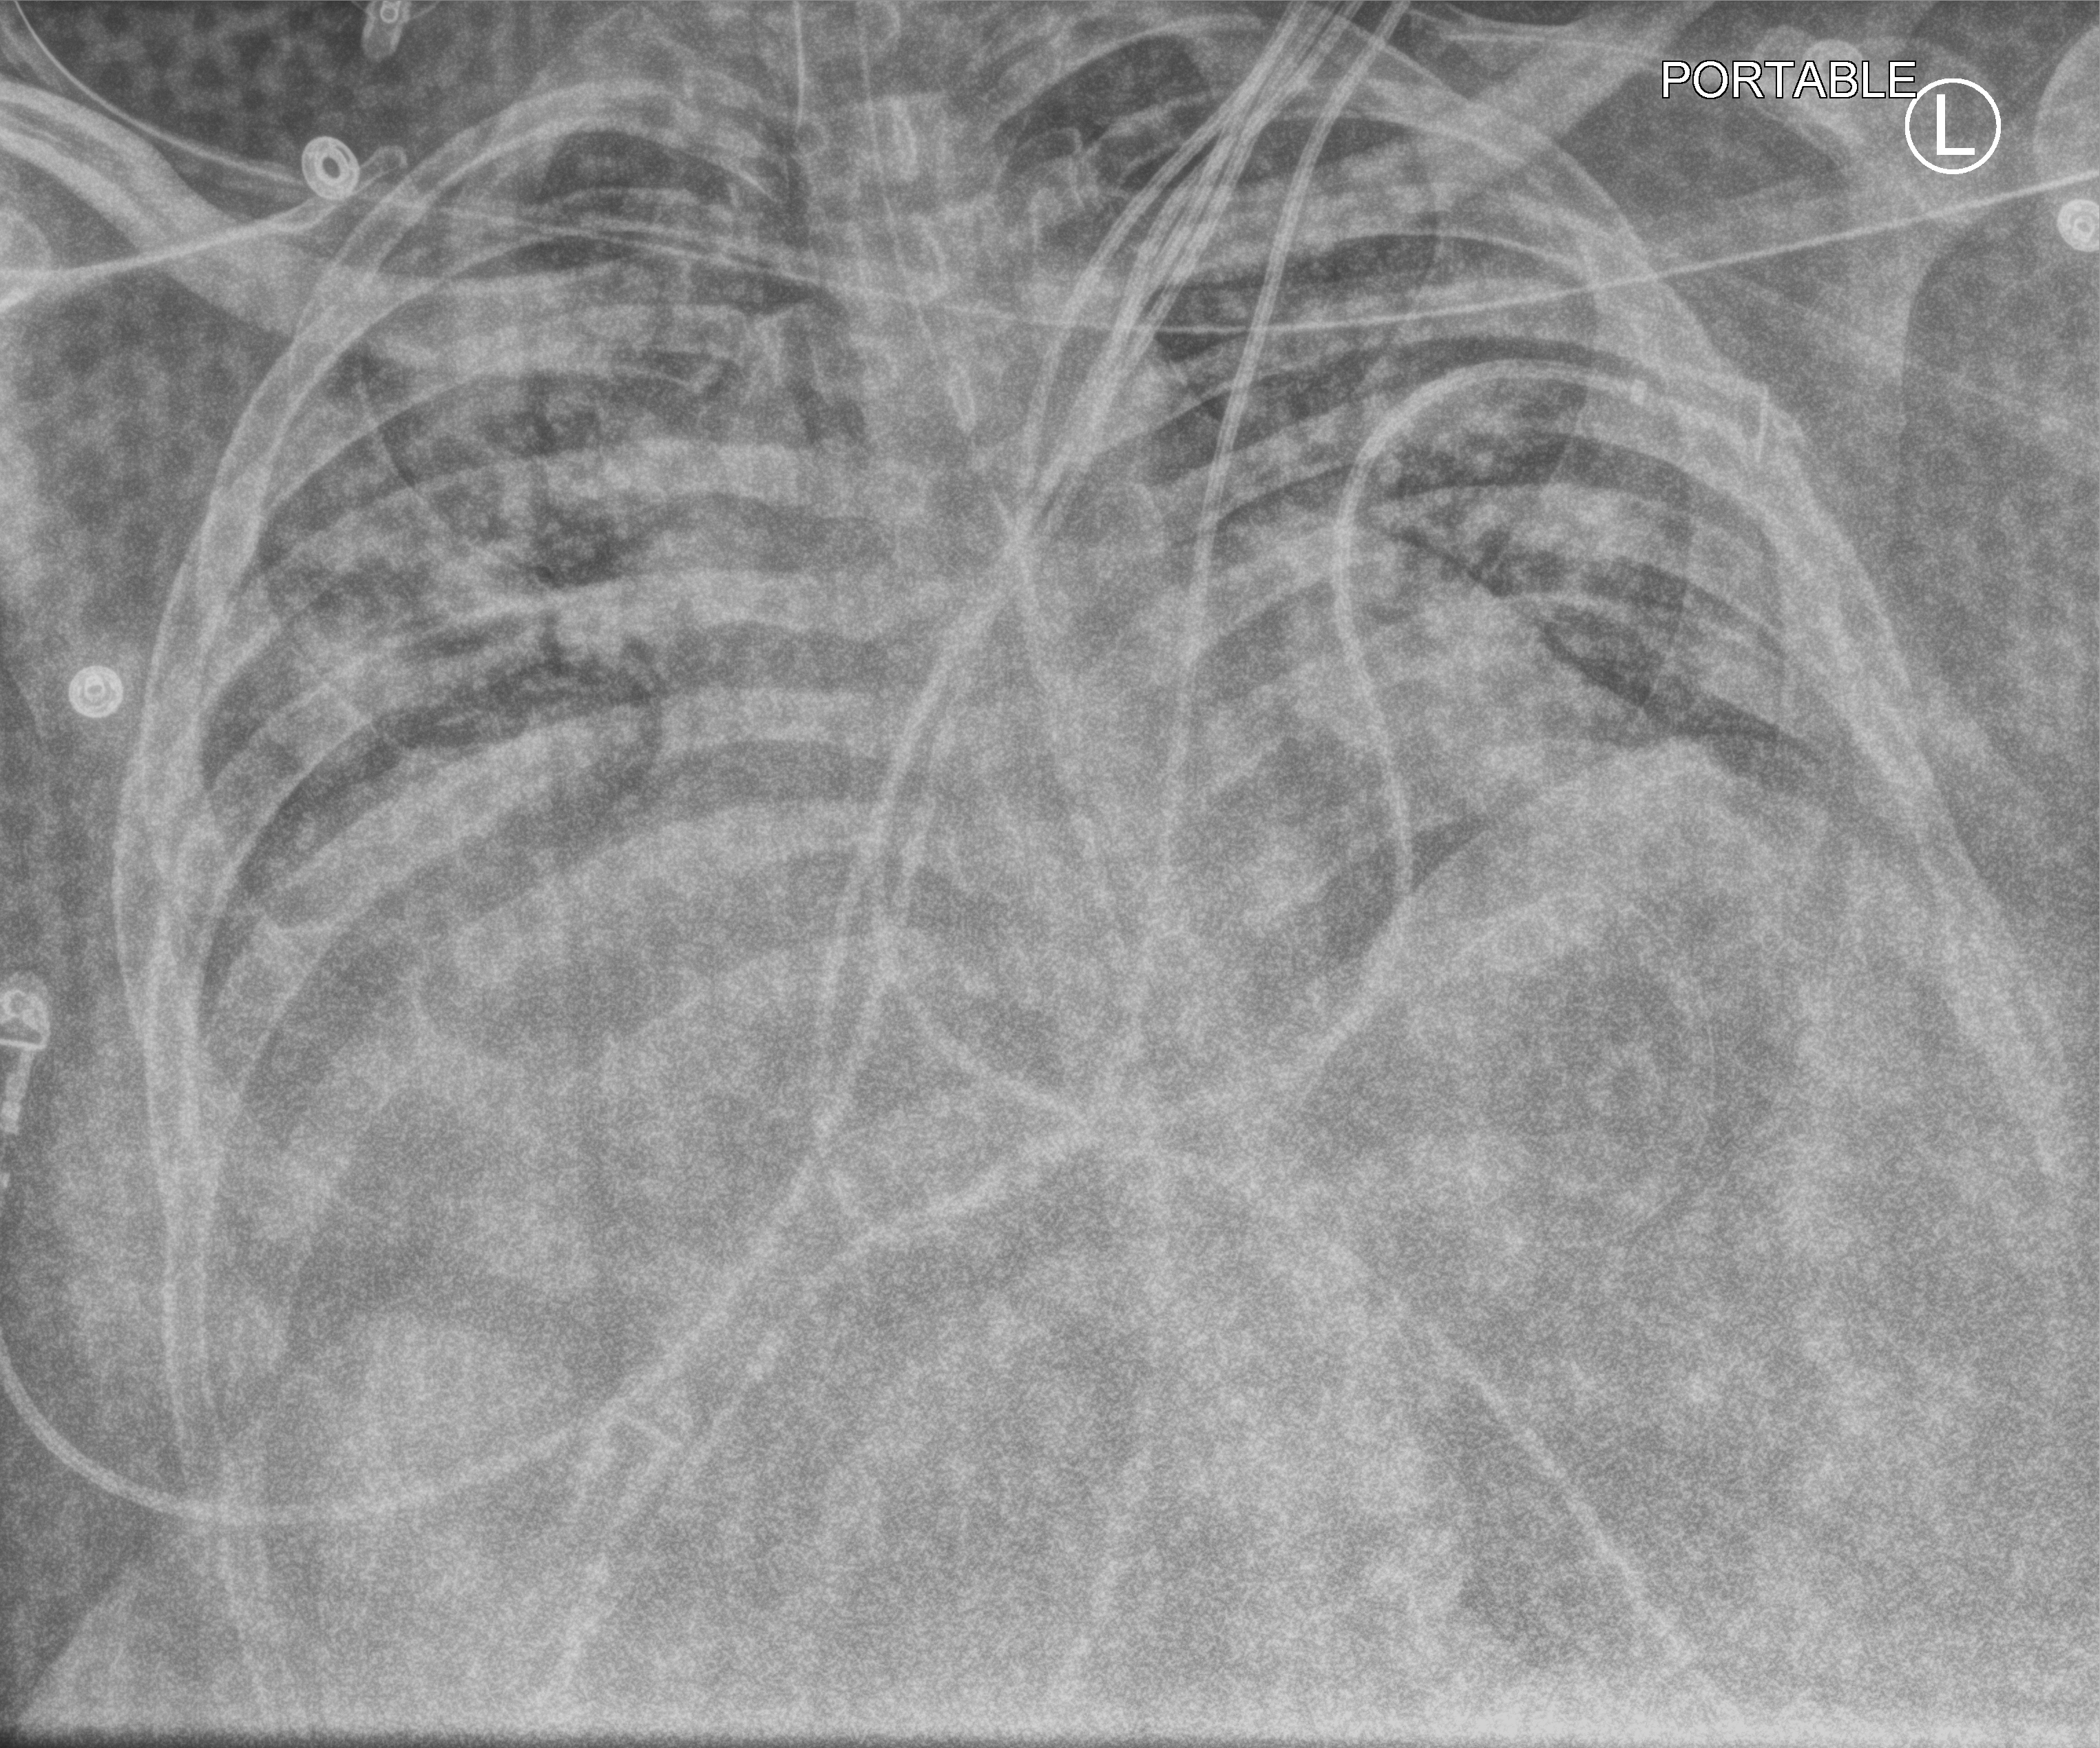
Portable chest radiograph; anteroposterior (AP) projection. Patient hospitalised with COVID-19; male, aged 18–59 years.
Hospital-stay facts (about this admission, not read from this image; timing relative to this image not recorded): mechanically ventilated during this hospital stay: yes.